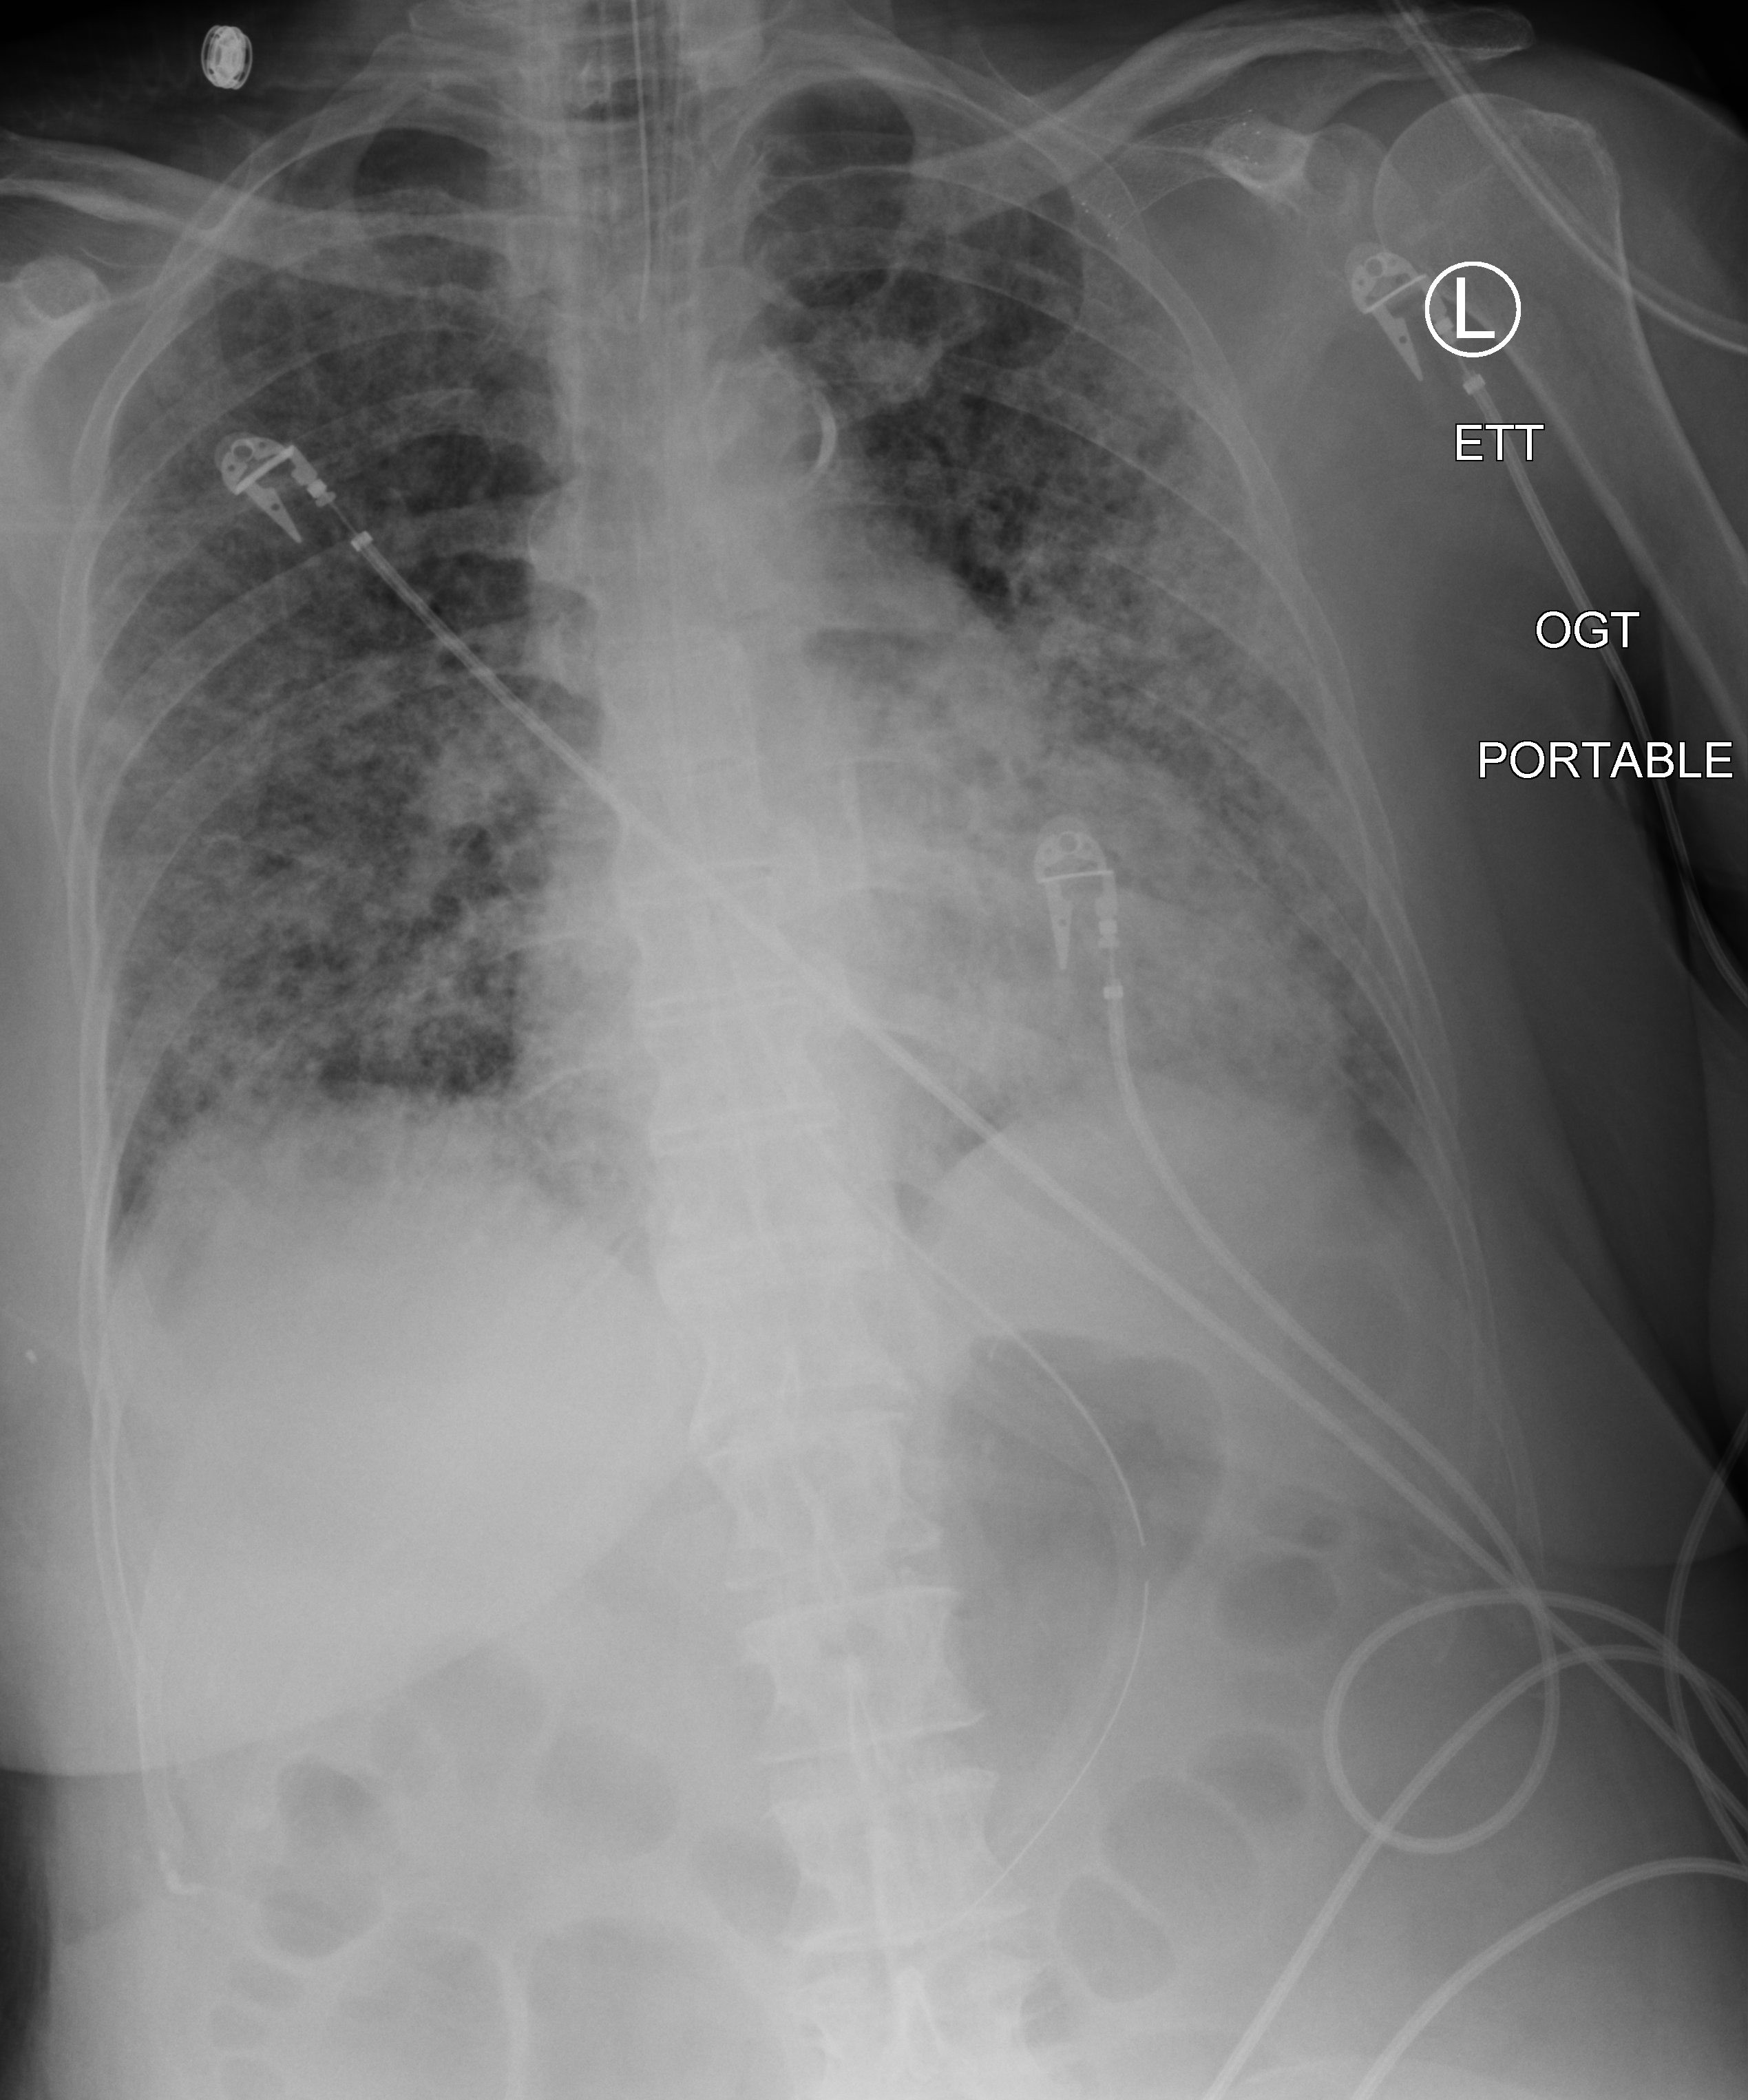
Portable chest radiograph. Patient hospitalised with COVID-19; female, aged 60–74 years.
From the hospital-stay record, not from the radiograph (when in the stay this image was taken is not recorded):
- admitted to intensive care during this hospital stay: yes
- mechanically ventilated during this hospital stay: yes